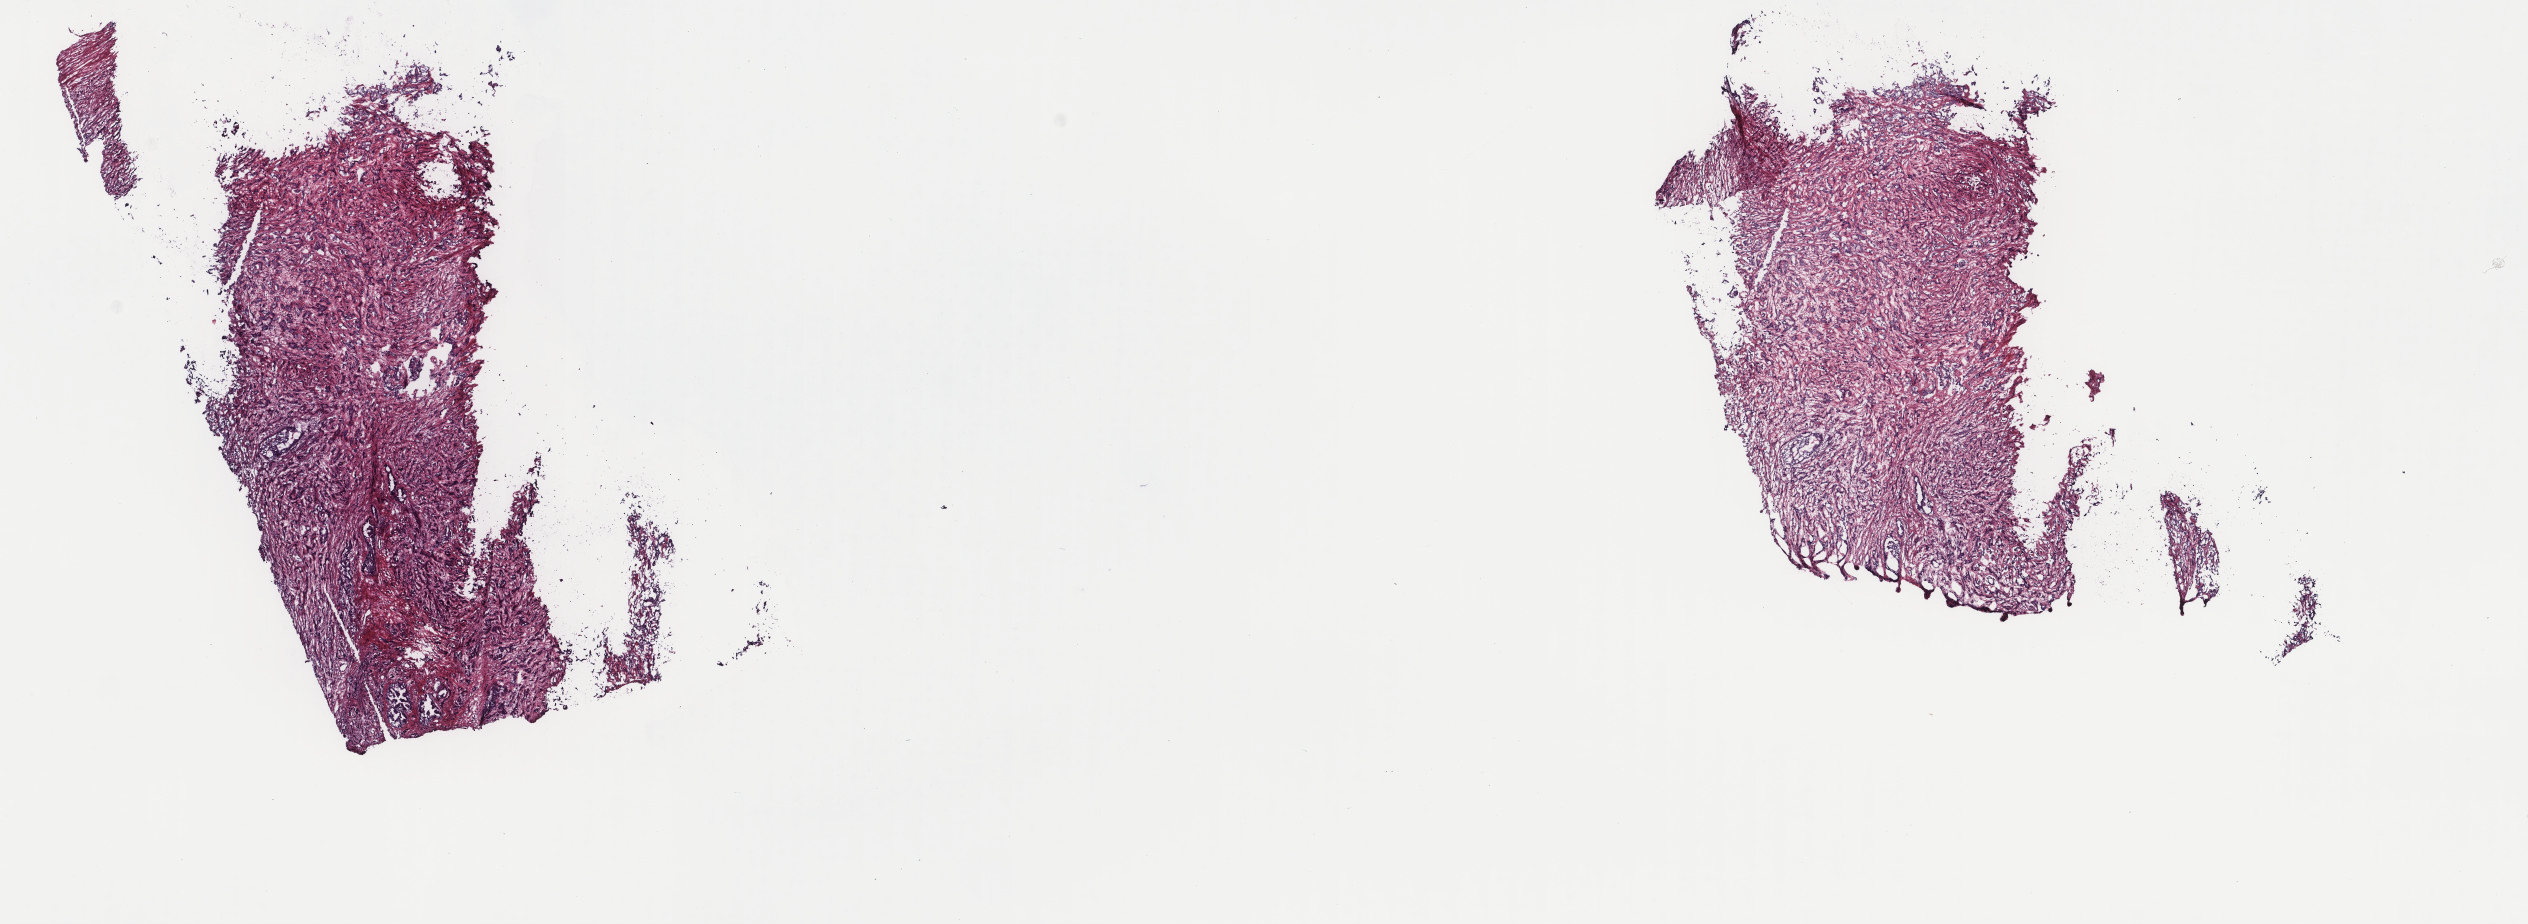
H&E whole-slide image — low-resolution overview of the scanned area, about 20.1 x 7.3 mm (slide scanned at 40x); frozen section; primary tumour sample from the prostate. Male patient; age at initial diagnosis 66 years. Gleason score: 9 (4+5). Composition of this section per pathologist review: tumour cells 60%, tumour nuclei 80%, normal cells 5%, stromal cells 35%, necrosis 0%. Infiltration values recorded for this section: lymphocyte infiltration 0%, monocyte infiltration 0%, neutrophil infiltration 0%.
Diagnosis: Adenocarcinoma, NOS (prostate gland). Lymph nodes positive (case pathology): 0 of 10 examined.